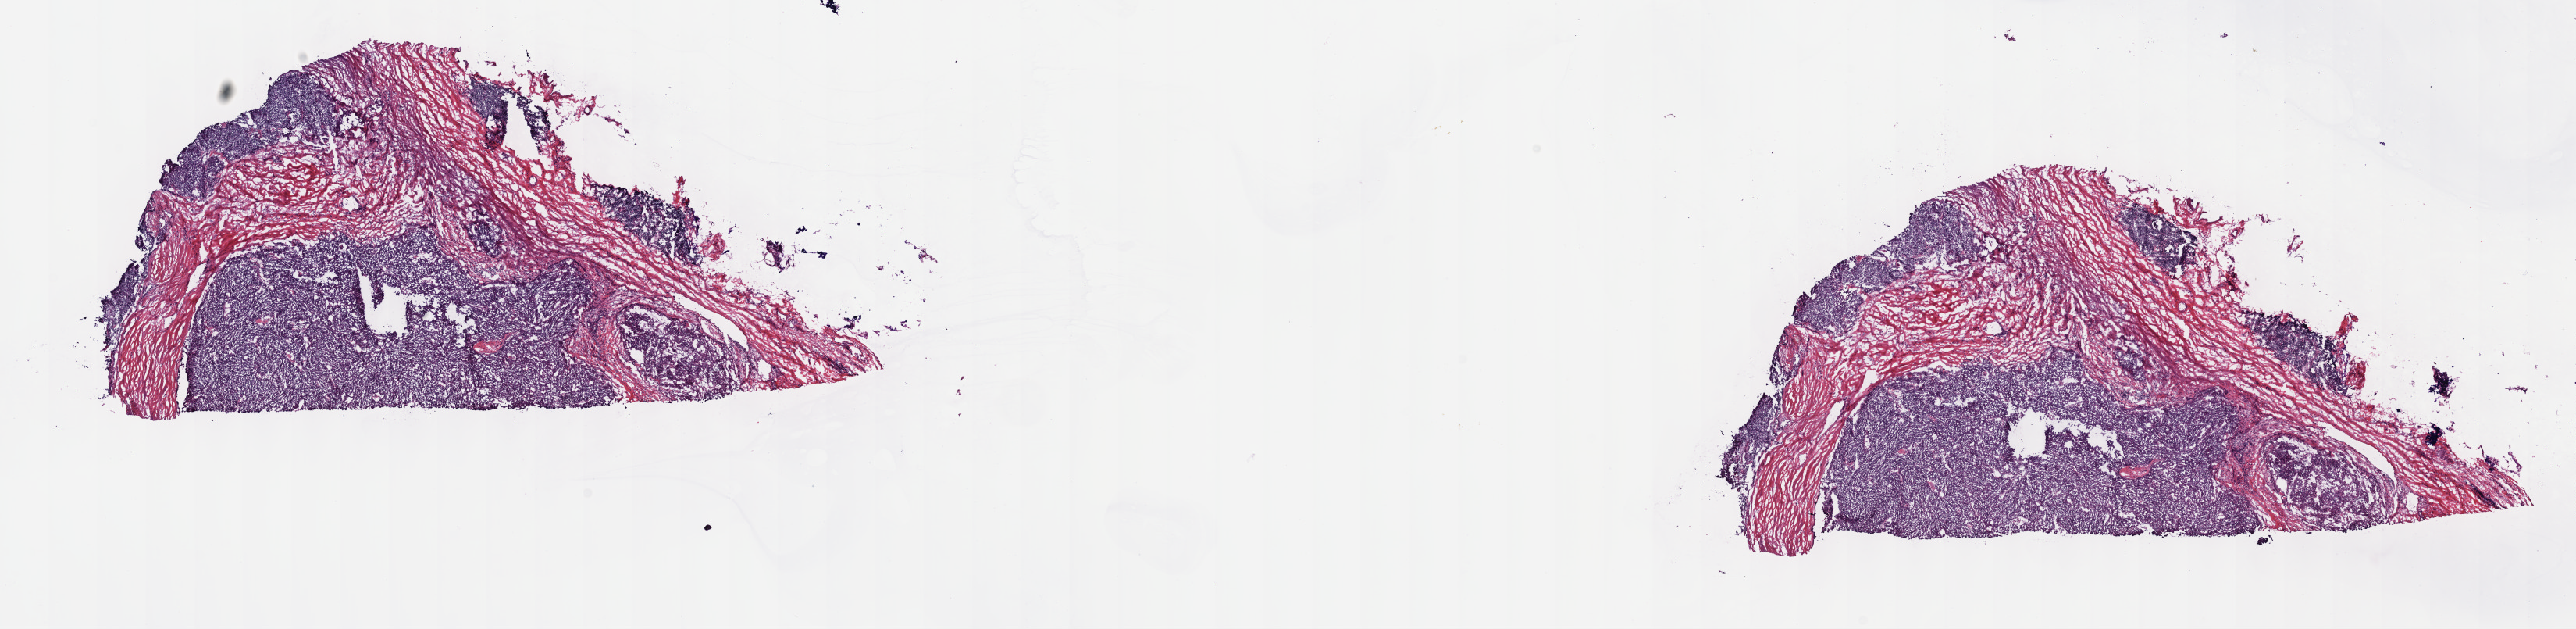
Digitized H&E-stained tissue section (whole slide) — low-resolution overview of the scanned area, about 26.7 x 6.5 mm; frozen section from the top of the tissue portion; thymus, primary tumour sample. Patient: male, age at initial diagnosis 77 years. Pathologist review of this section (percent, as recorded): tumour cells 50%, tumour nuclei 75%, normal cells 50%, stromal cells 0%, necrosis 0%. Infiltration values recorded for this section: lymphocyte infiltration 1%, monocyte infiltration 0%, neutrophil infiltration 0%.
Diagnosis: Thymoma, type B2, malignant.